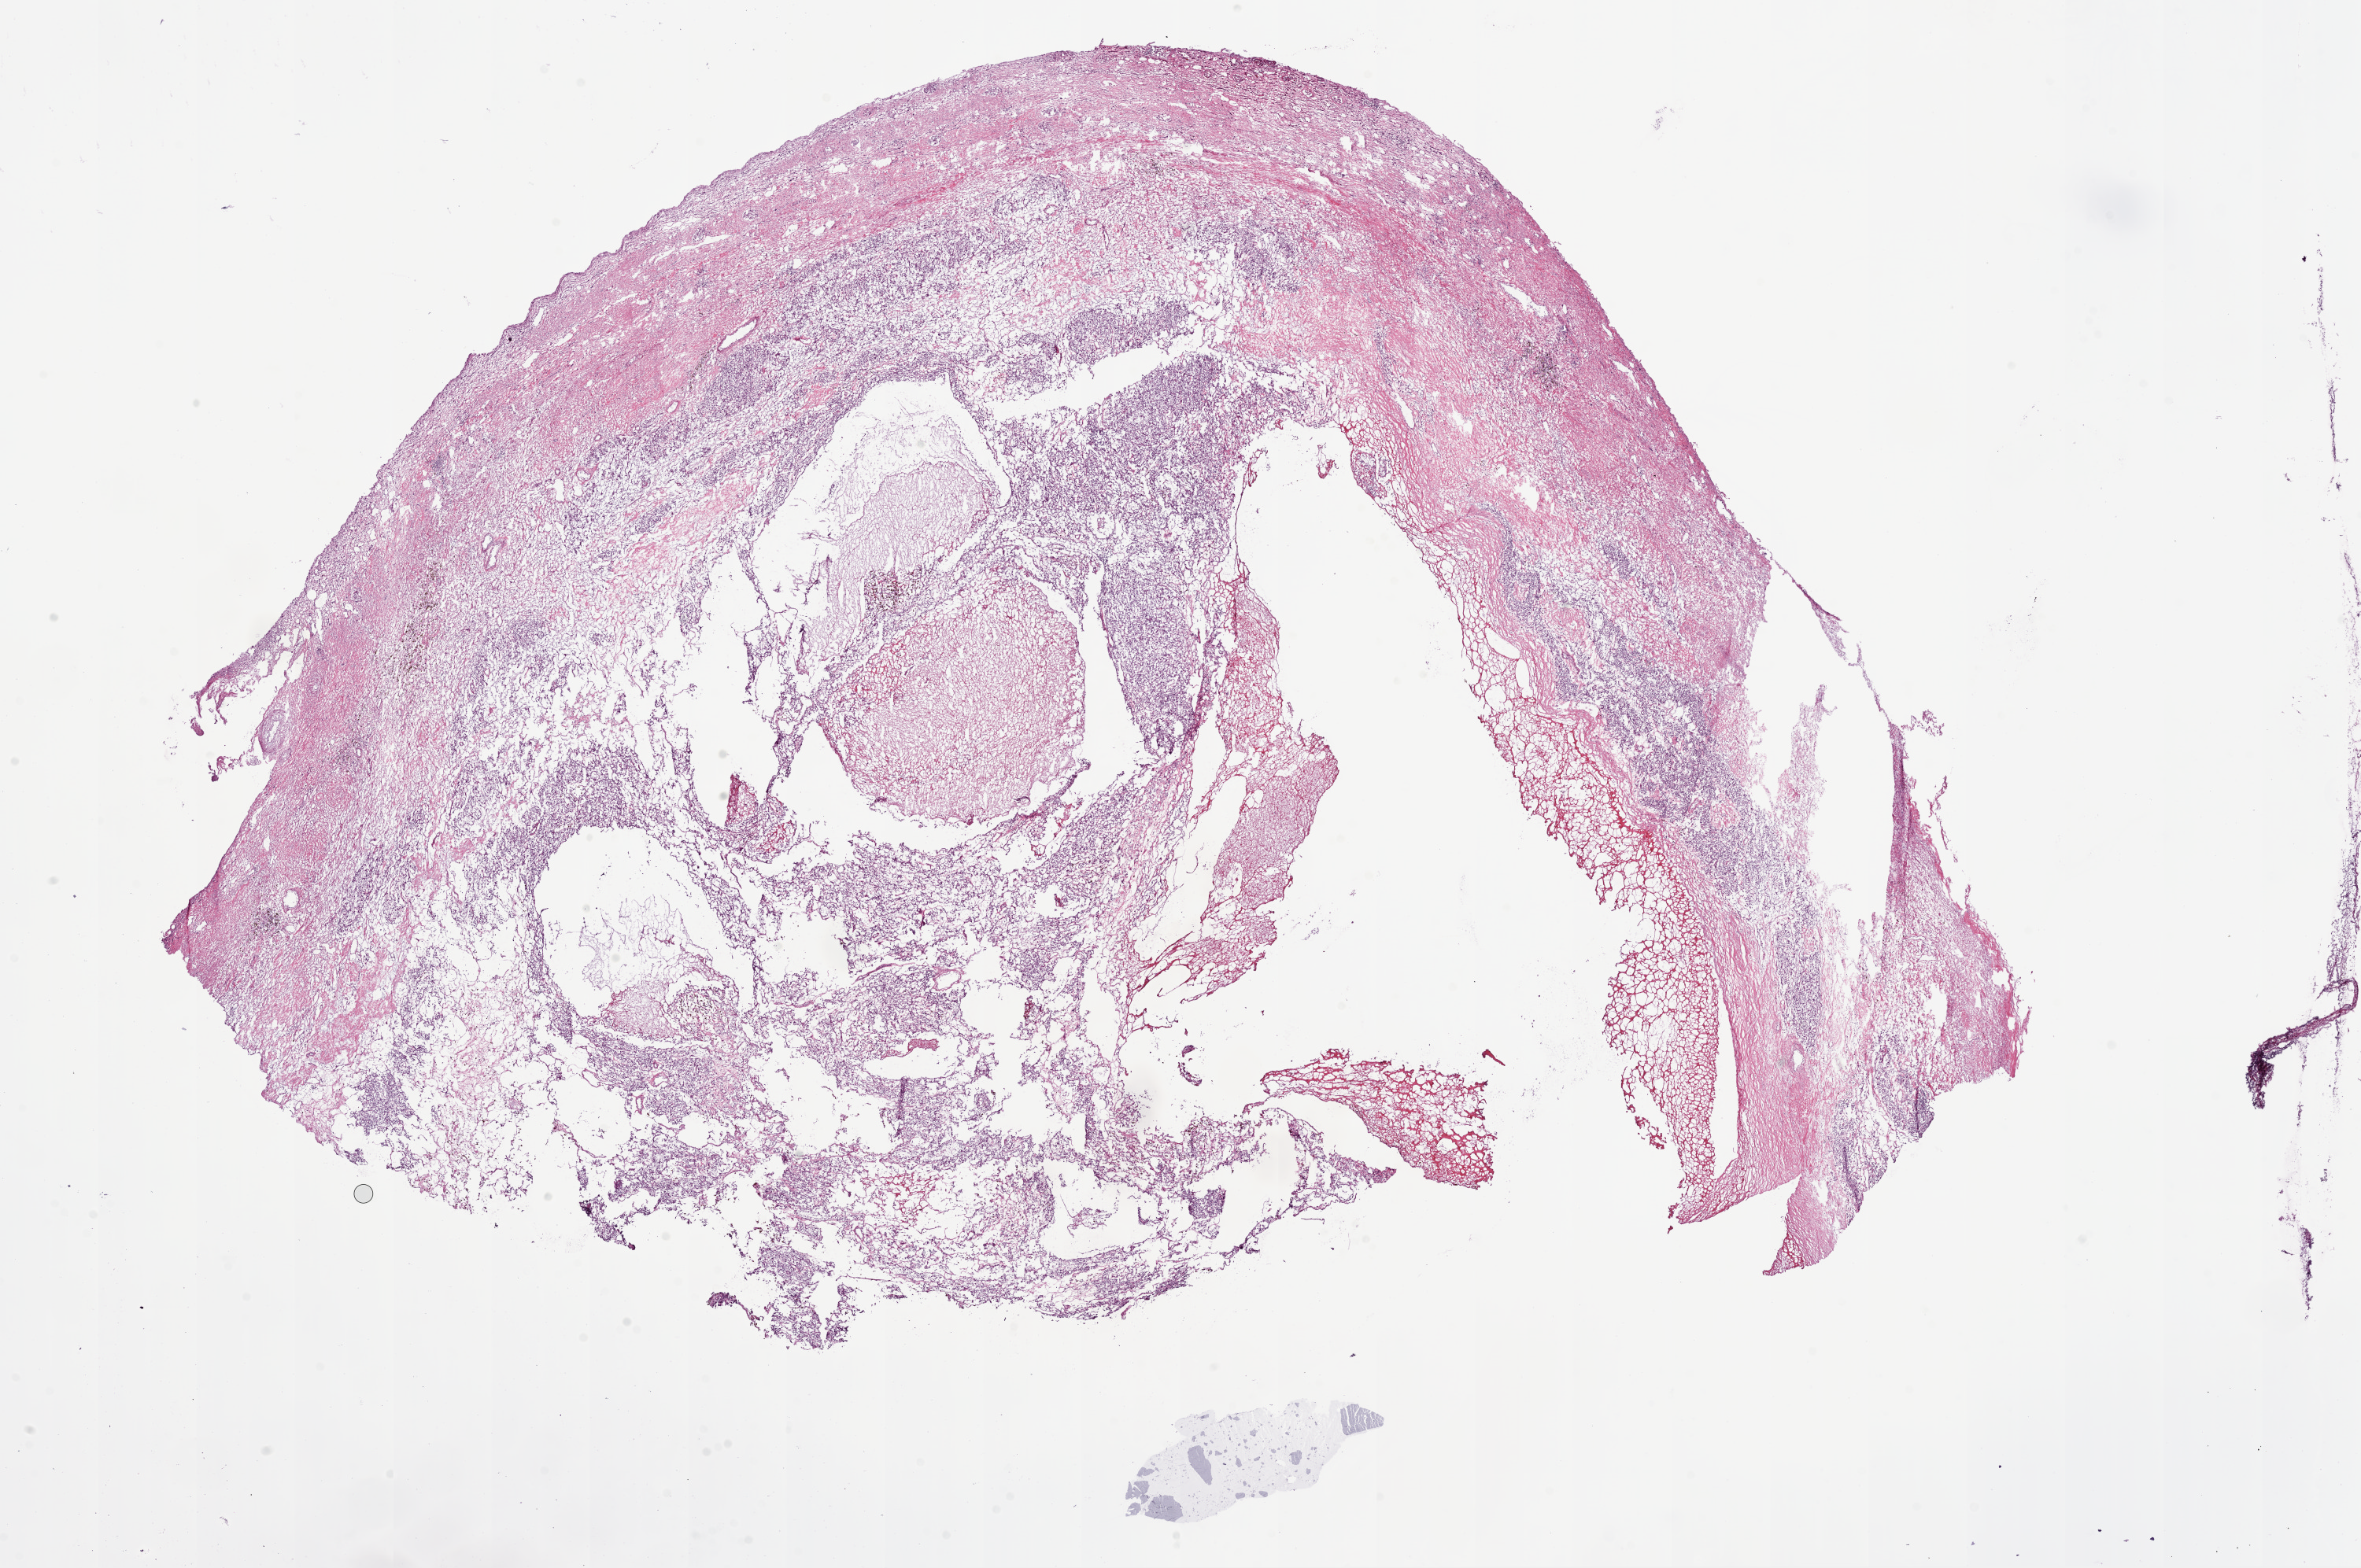
H&E whole-slide image — shown as a low-resolution overview of the whole scanned area (about 24.1 x 16.0 mm). Frozen section from the bottom of the tissue portion. Primary tumour sample from the kidney. Patient: male, age at initial diagnosis 37 years. Histologic grade: G2 (moderately differentiated). Pathologist review of this section (percent, as recorded): tumour cells 55%, tumour nuclei 70%, normal cells 10%, stromal cells 35%, necrosis 0%.
• diagnosis: Clear cell adenocarcinoma, NOS
• AJCC pathologic stage: I